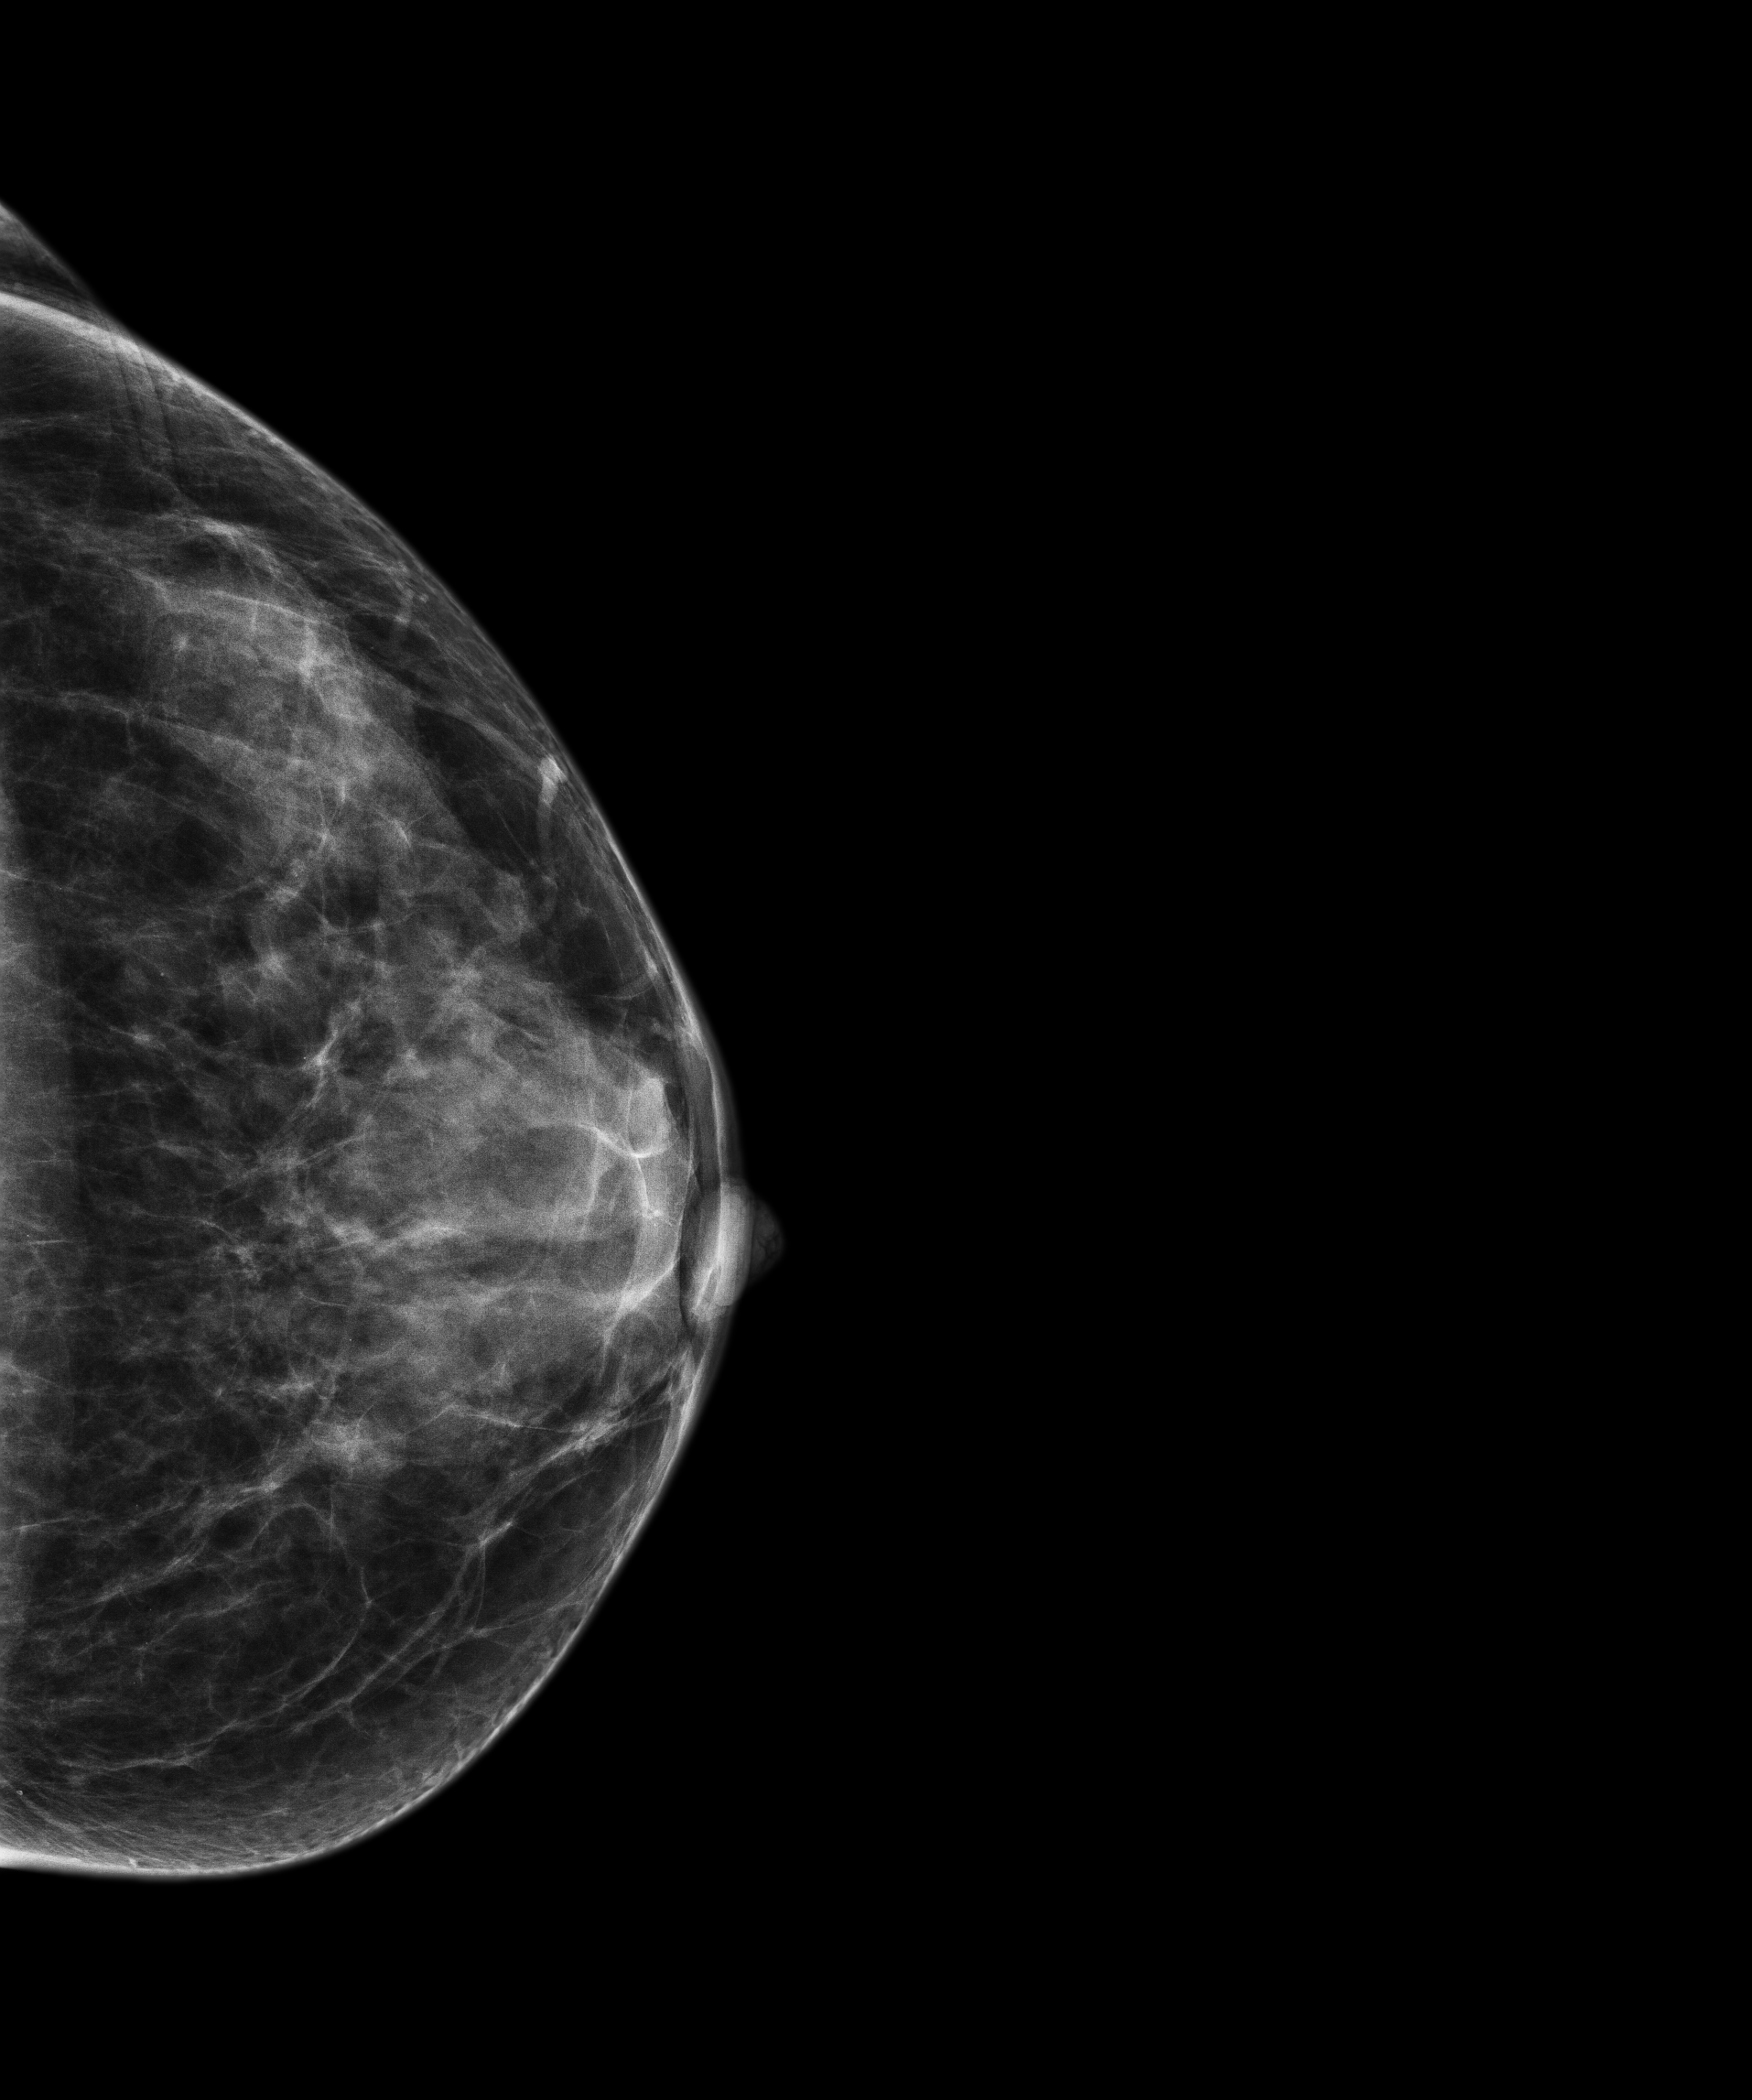
Digital mammogram (FFDM), left breast, craniocaudal (CC) view, annual screening mammography examination, system: Senographe Pristina. Patient: female, 48 years.
Final BI-RADS category for the screening round (tomosynthesis exam, both breasts): category 2.